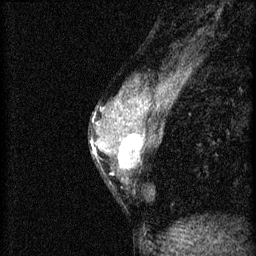
Breast MRI (dynamic contrast-enhanced), one sagittal slice; slice 27 of 46 in the series (ordered by position); 3 images stored at this slice position (order not interpretable as contrast timing); 1.5 T; TE 4.2 ms, TR 8.2 ms; 2 mm slice thickness; 256 × 256 image matrix, field of view 180 × 180 mm. Female patient, age 44 years.
Structures marked on this image (semi-automatically segmented with operator editing):
- analysis volume of interest (the breast-tissue region the enhancement analysis was run in; not a lesion): bounding box <110,128,156,179> (left, top, right, bottom; pixels)
- tumour enhancement mask (voxels above the 70 % enhancement threshold inside the analysis volume of interest): <111,132,146,175>